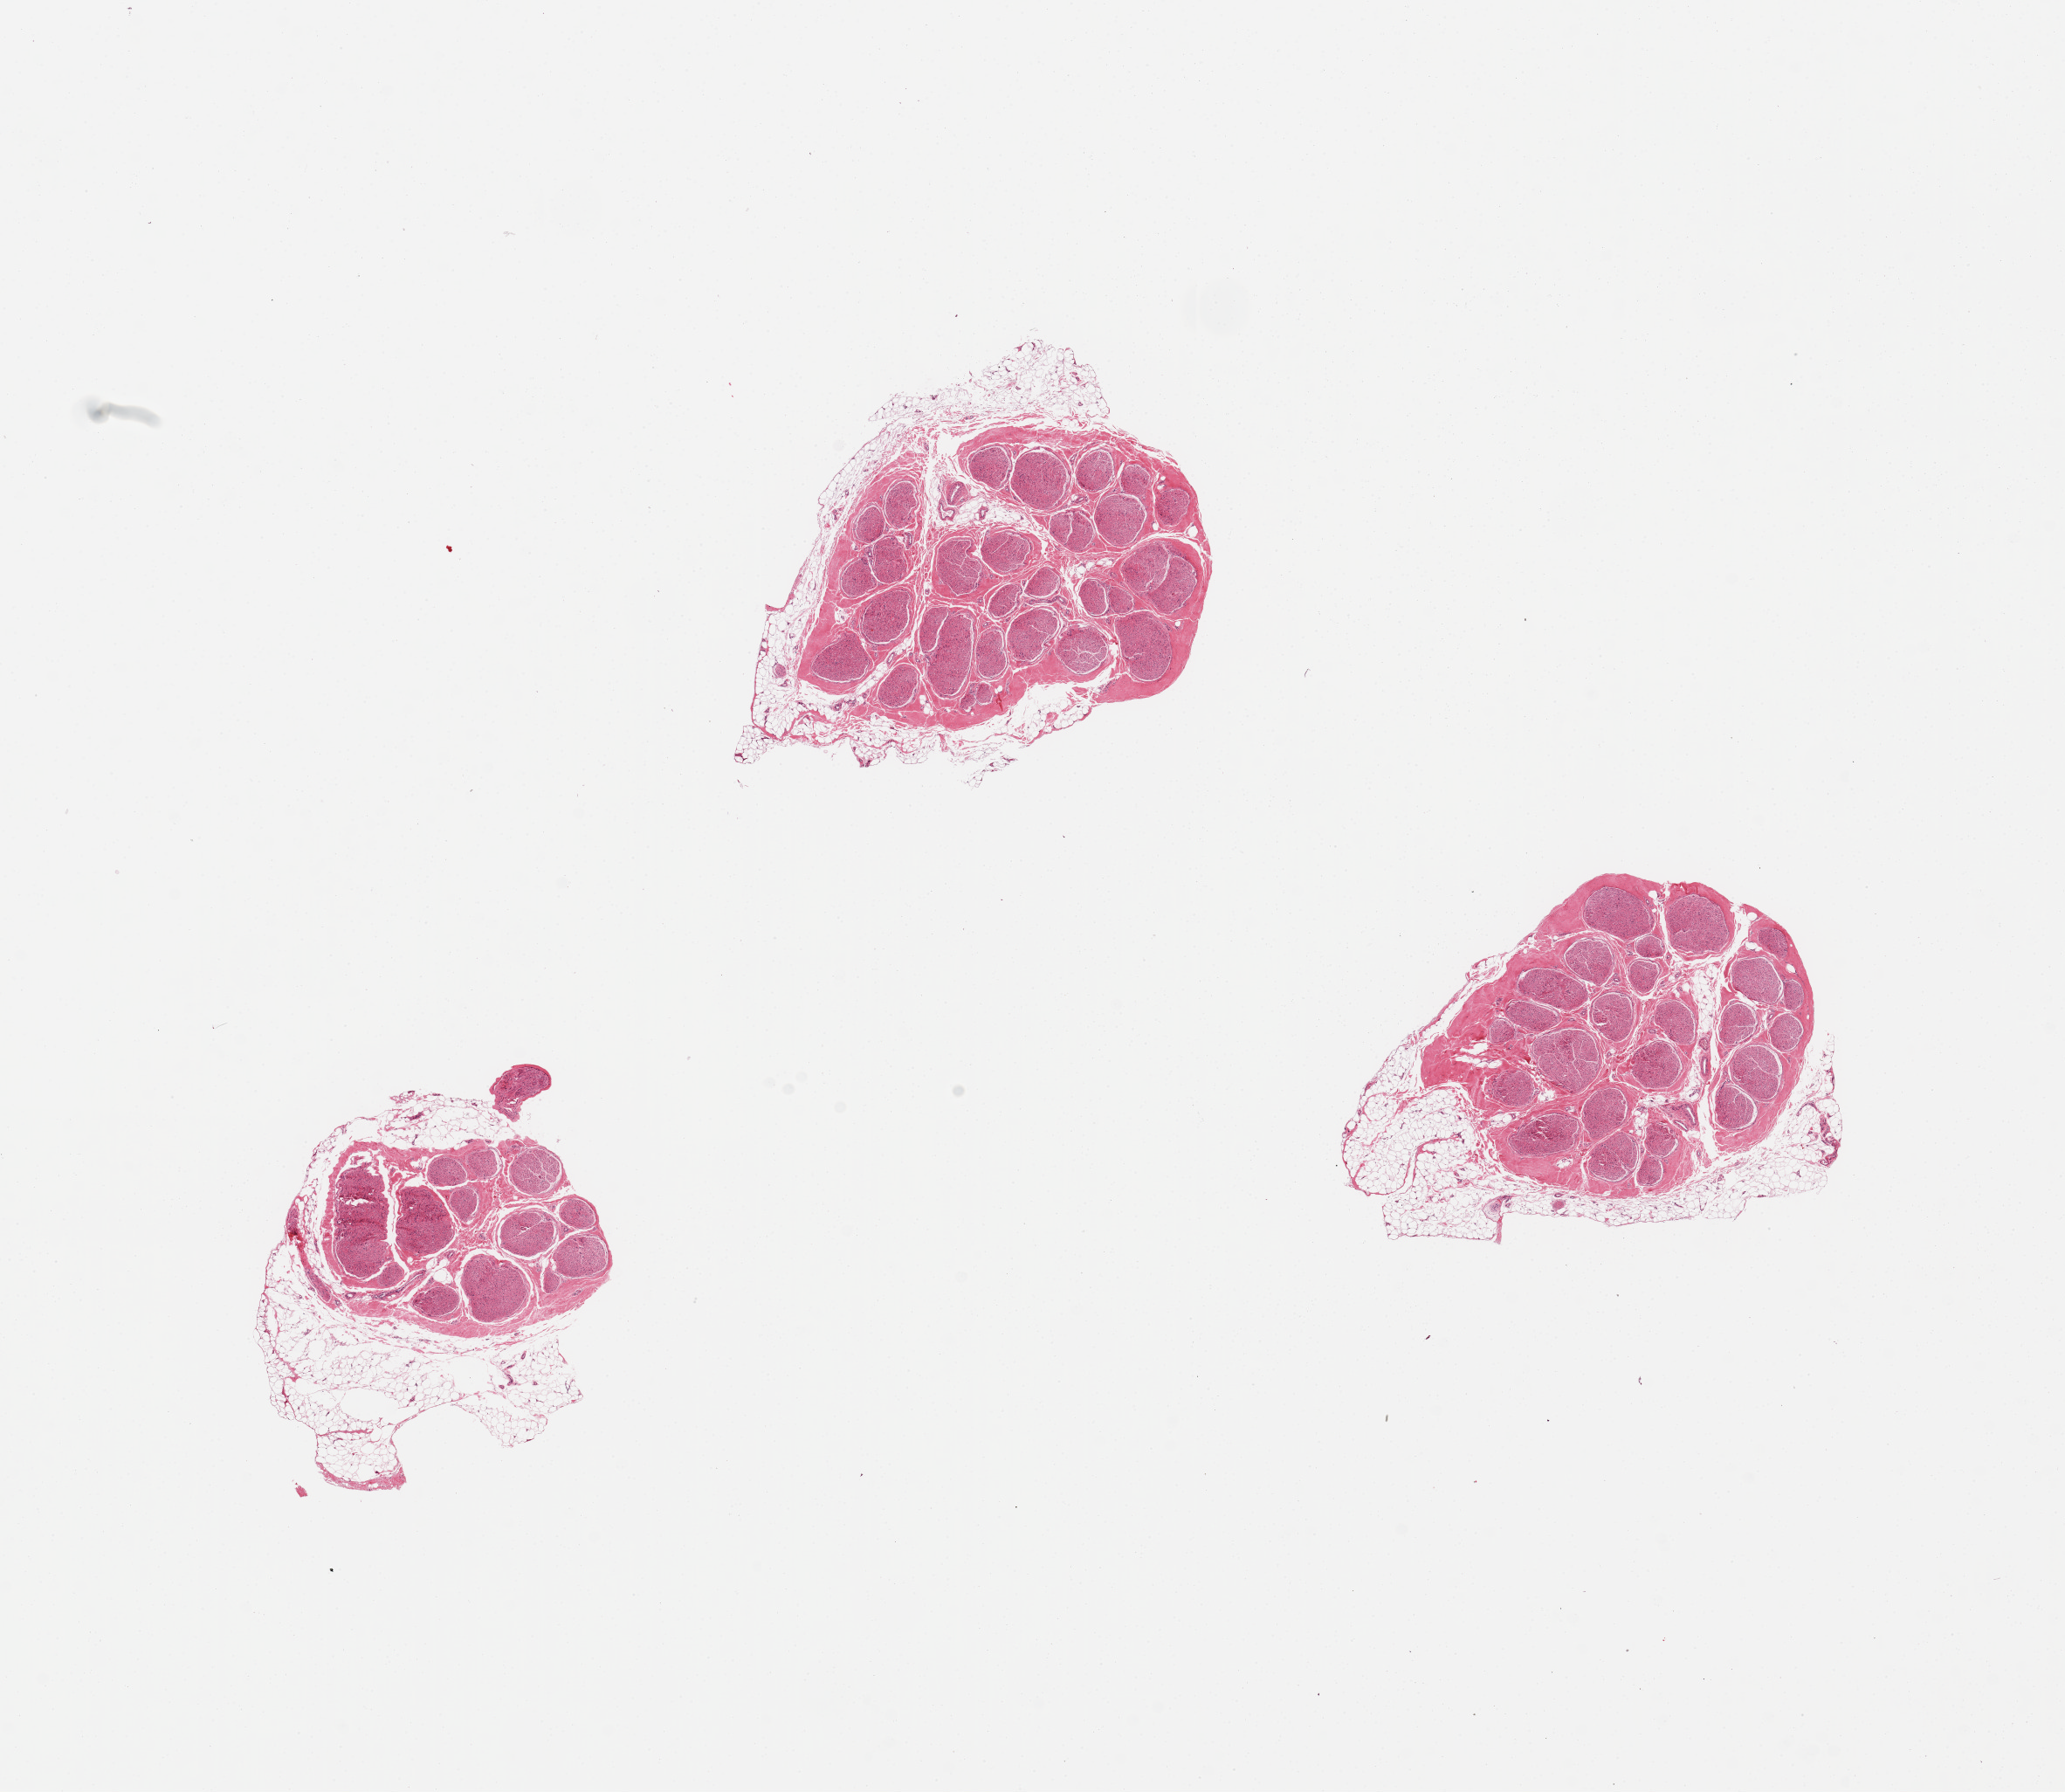
Hematoxylin and eosin (H&E) whole-slide image — a low-resolution overview of the entire scanned area, about 18.7 x 16.2 mm (acquisition: 20x scan). PAXgene-fixed paraffin-embedded (PFPE) section. Sampled site (target tissue): tibial nerve. Donor tissue sample. Donor: female.
• pathologist's review note for this sample: 3 pieces, adherent discontinous rims of fat up to ~1.3mm